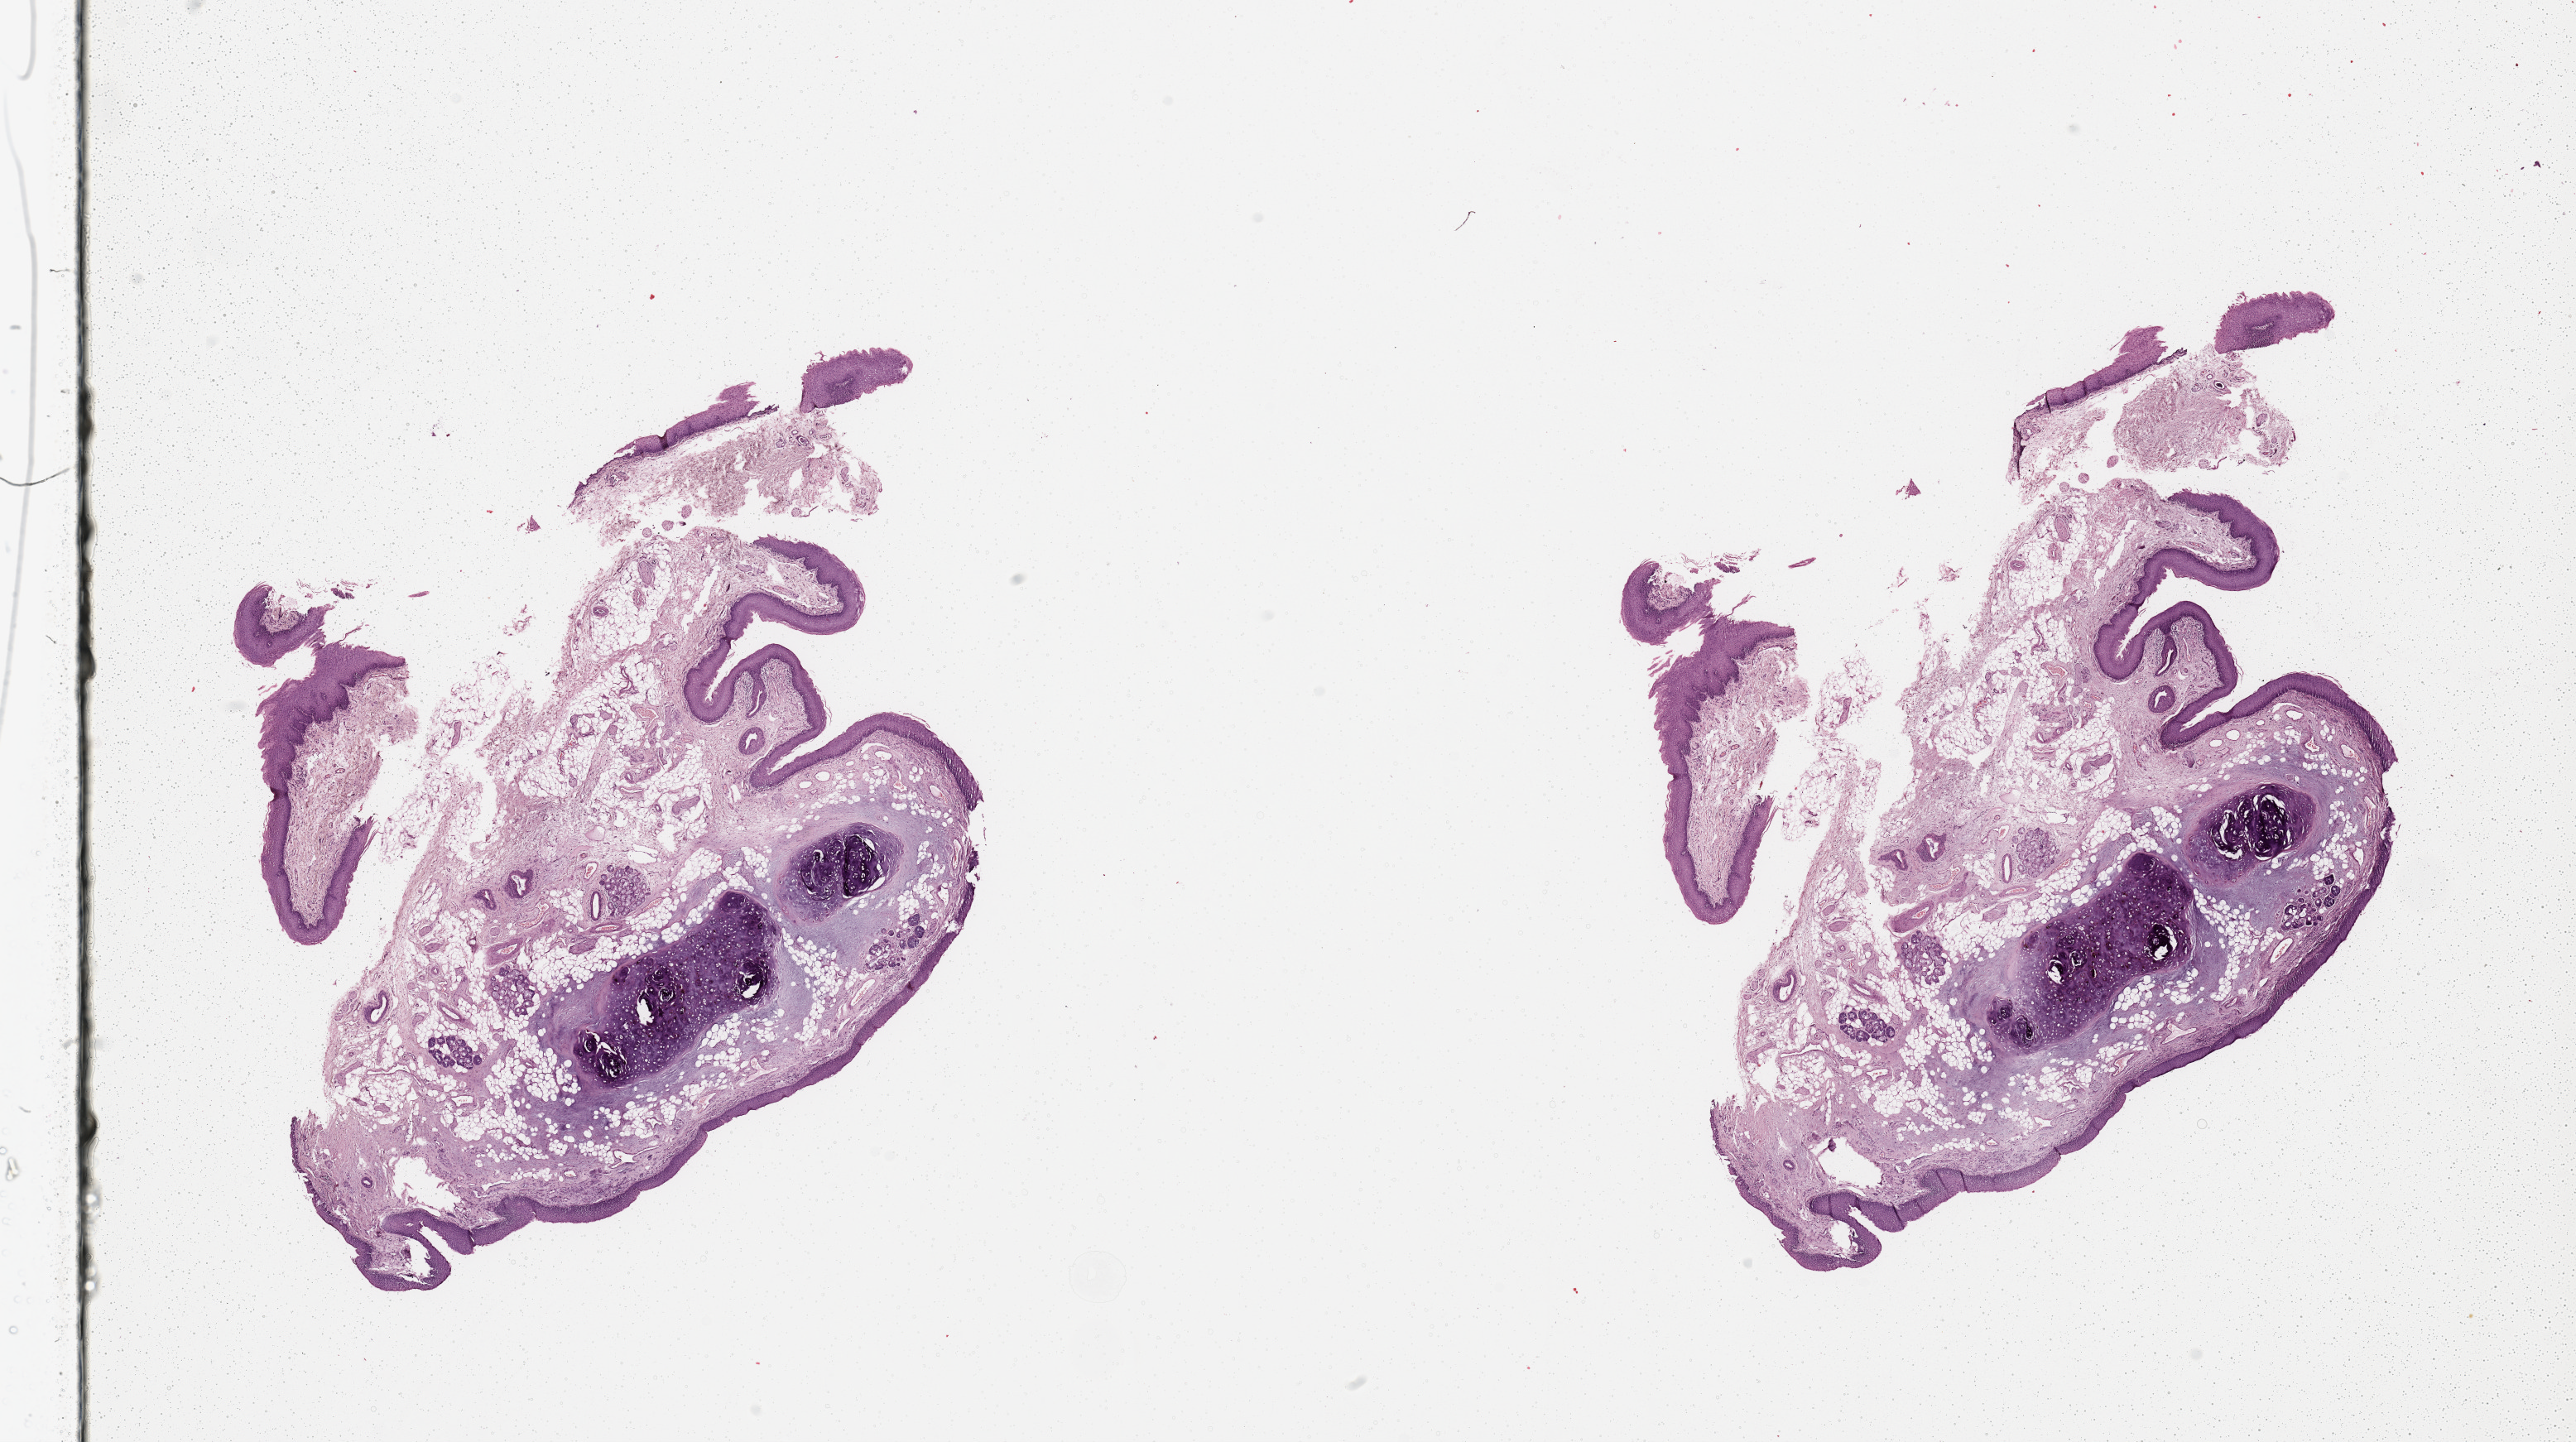
Whole-slide histology image, Hematoxylin and eosin (H&E) stained, a low-resolution overview of the entire scanned area, about 24.6 x 13.8 mm, normal (non-tumour) tissue sample, sampled site: larynx. Male, 58 y/o.
This section: normal (non-tumour) tissue from the same patient. Patient diagnosis: Squamous cell carcinoma, NOS (larynx, NOS).